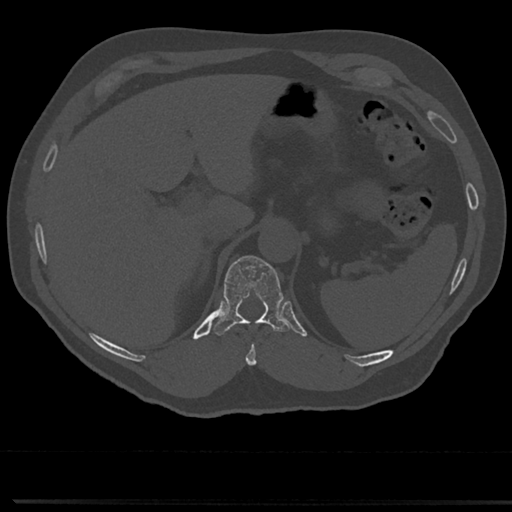
CT including the spine, one axial slice. Slice 213 of 817 in the series (ordered by position). Bone window (W 1800 / L 400 HU). 0.5 mm slice thickness. 512 × 512 image matrix, field of view 355 × 355 mm. Patient: male, 61 years. Case-level facts recorded for this patient, not image findings: primary cancer: prostate.
Outlined on this slice (semi-automatically segmented with operator editing):
- T10 vertebra: bounding box (x1, y1, x2, y2) in pixels: (246, 329, 260, 366)
- T11 vertebra: (214, 256, 288, 335)